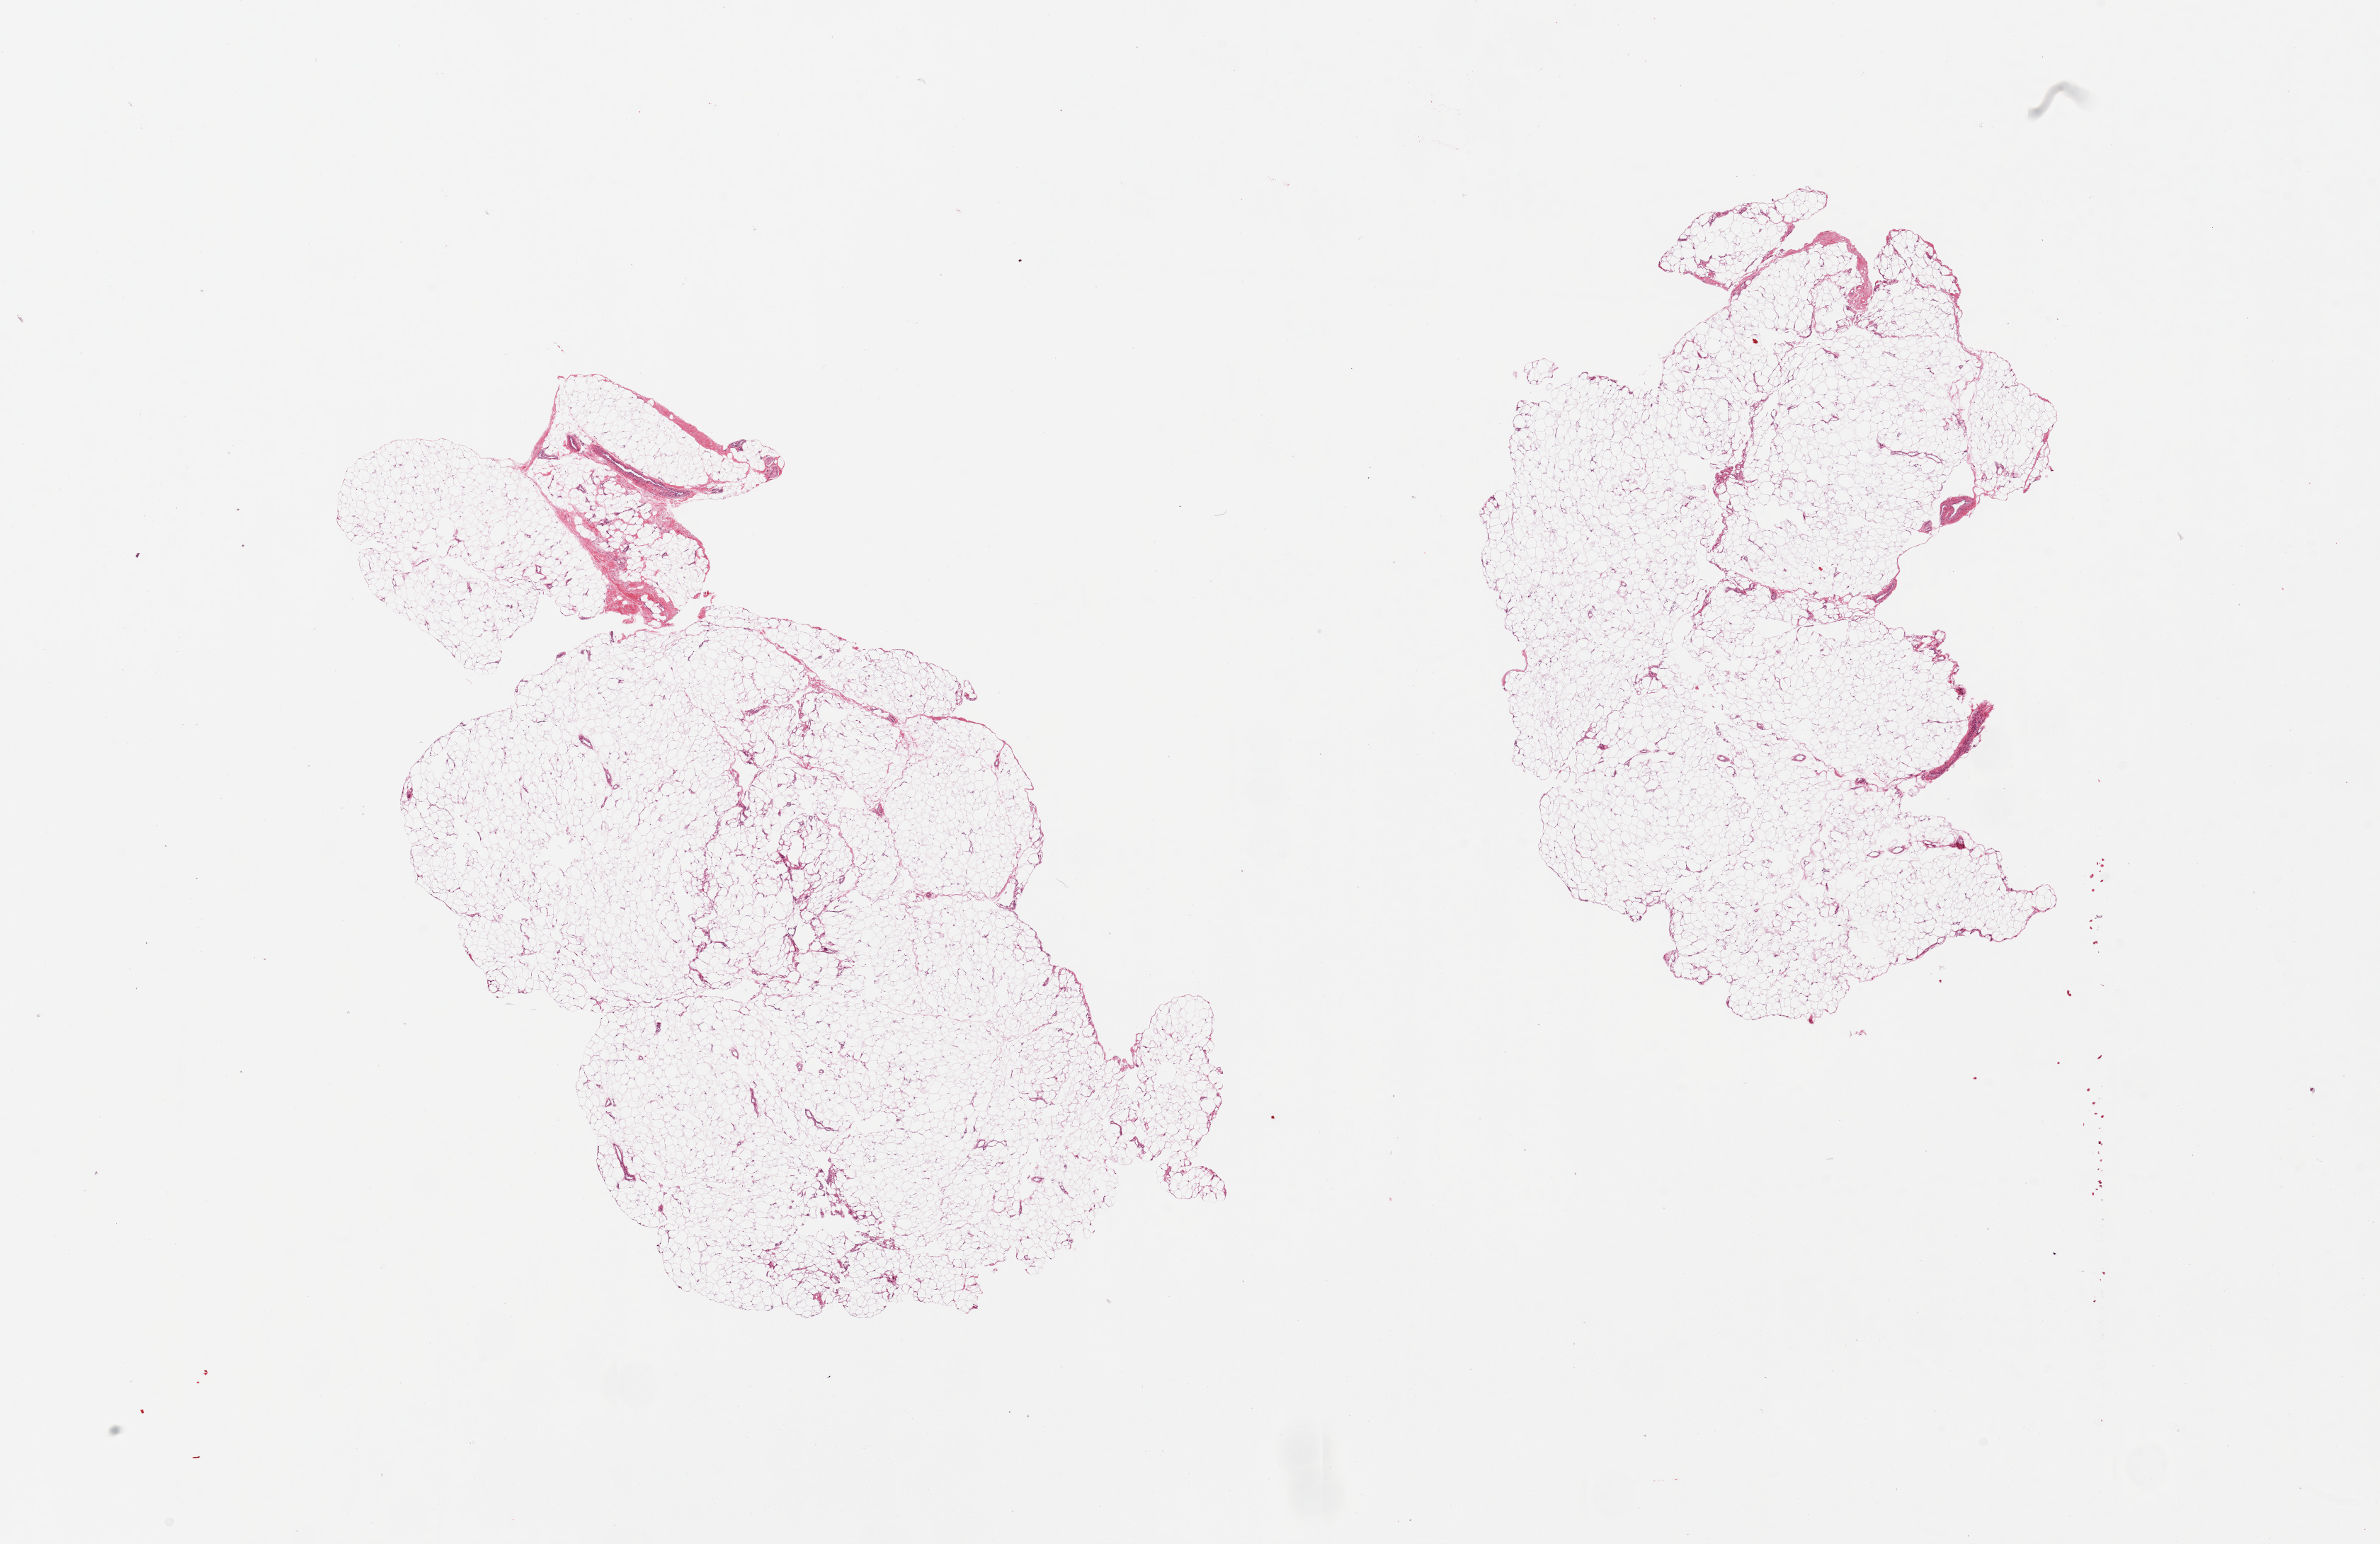
Whole-slide image, H&E stain, whole scanned area (about 26.6 x 17.2 mm, from a 20x scan) shown as a low-resolution overview. PAXgene-fixed, paraffin-embedded tissue. Target tissue: adipose tissue. Tissue donor sample.
Reviewer comment on this tissue sample: 1 pieces.